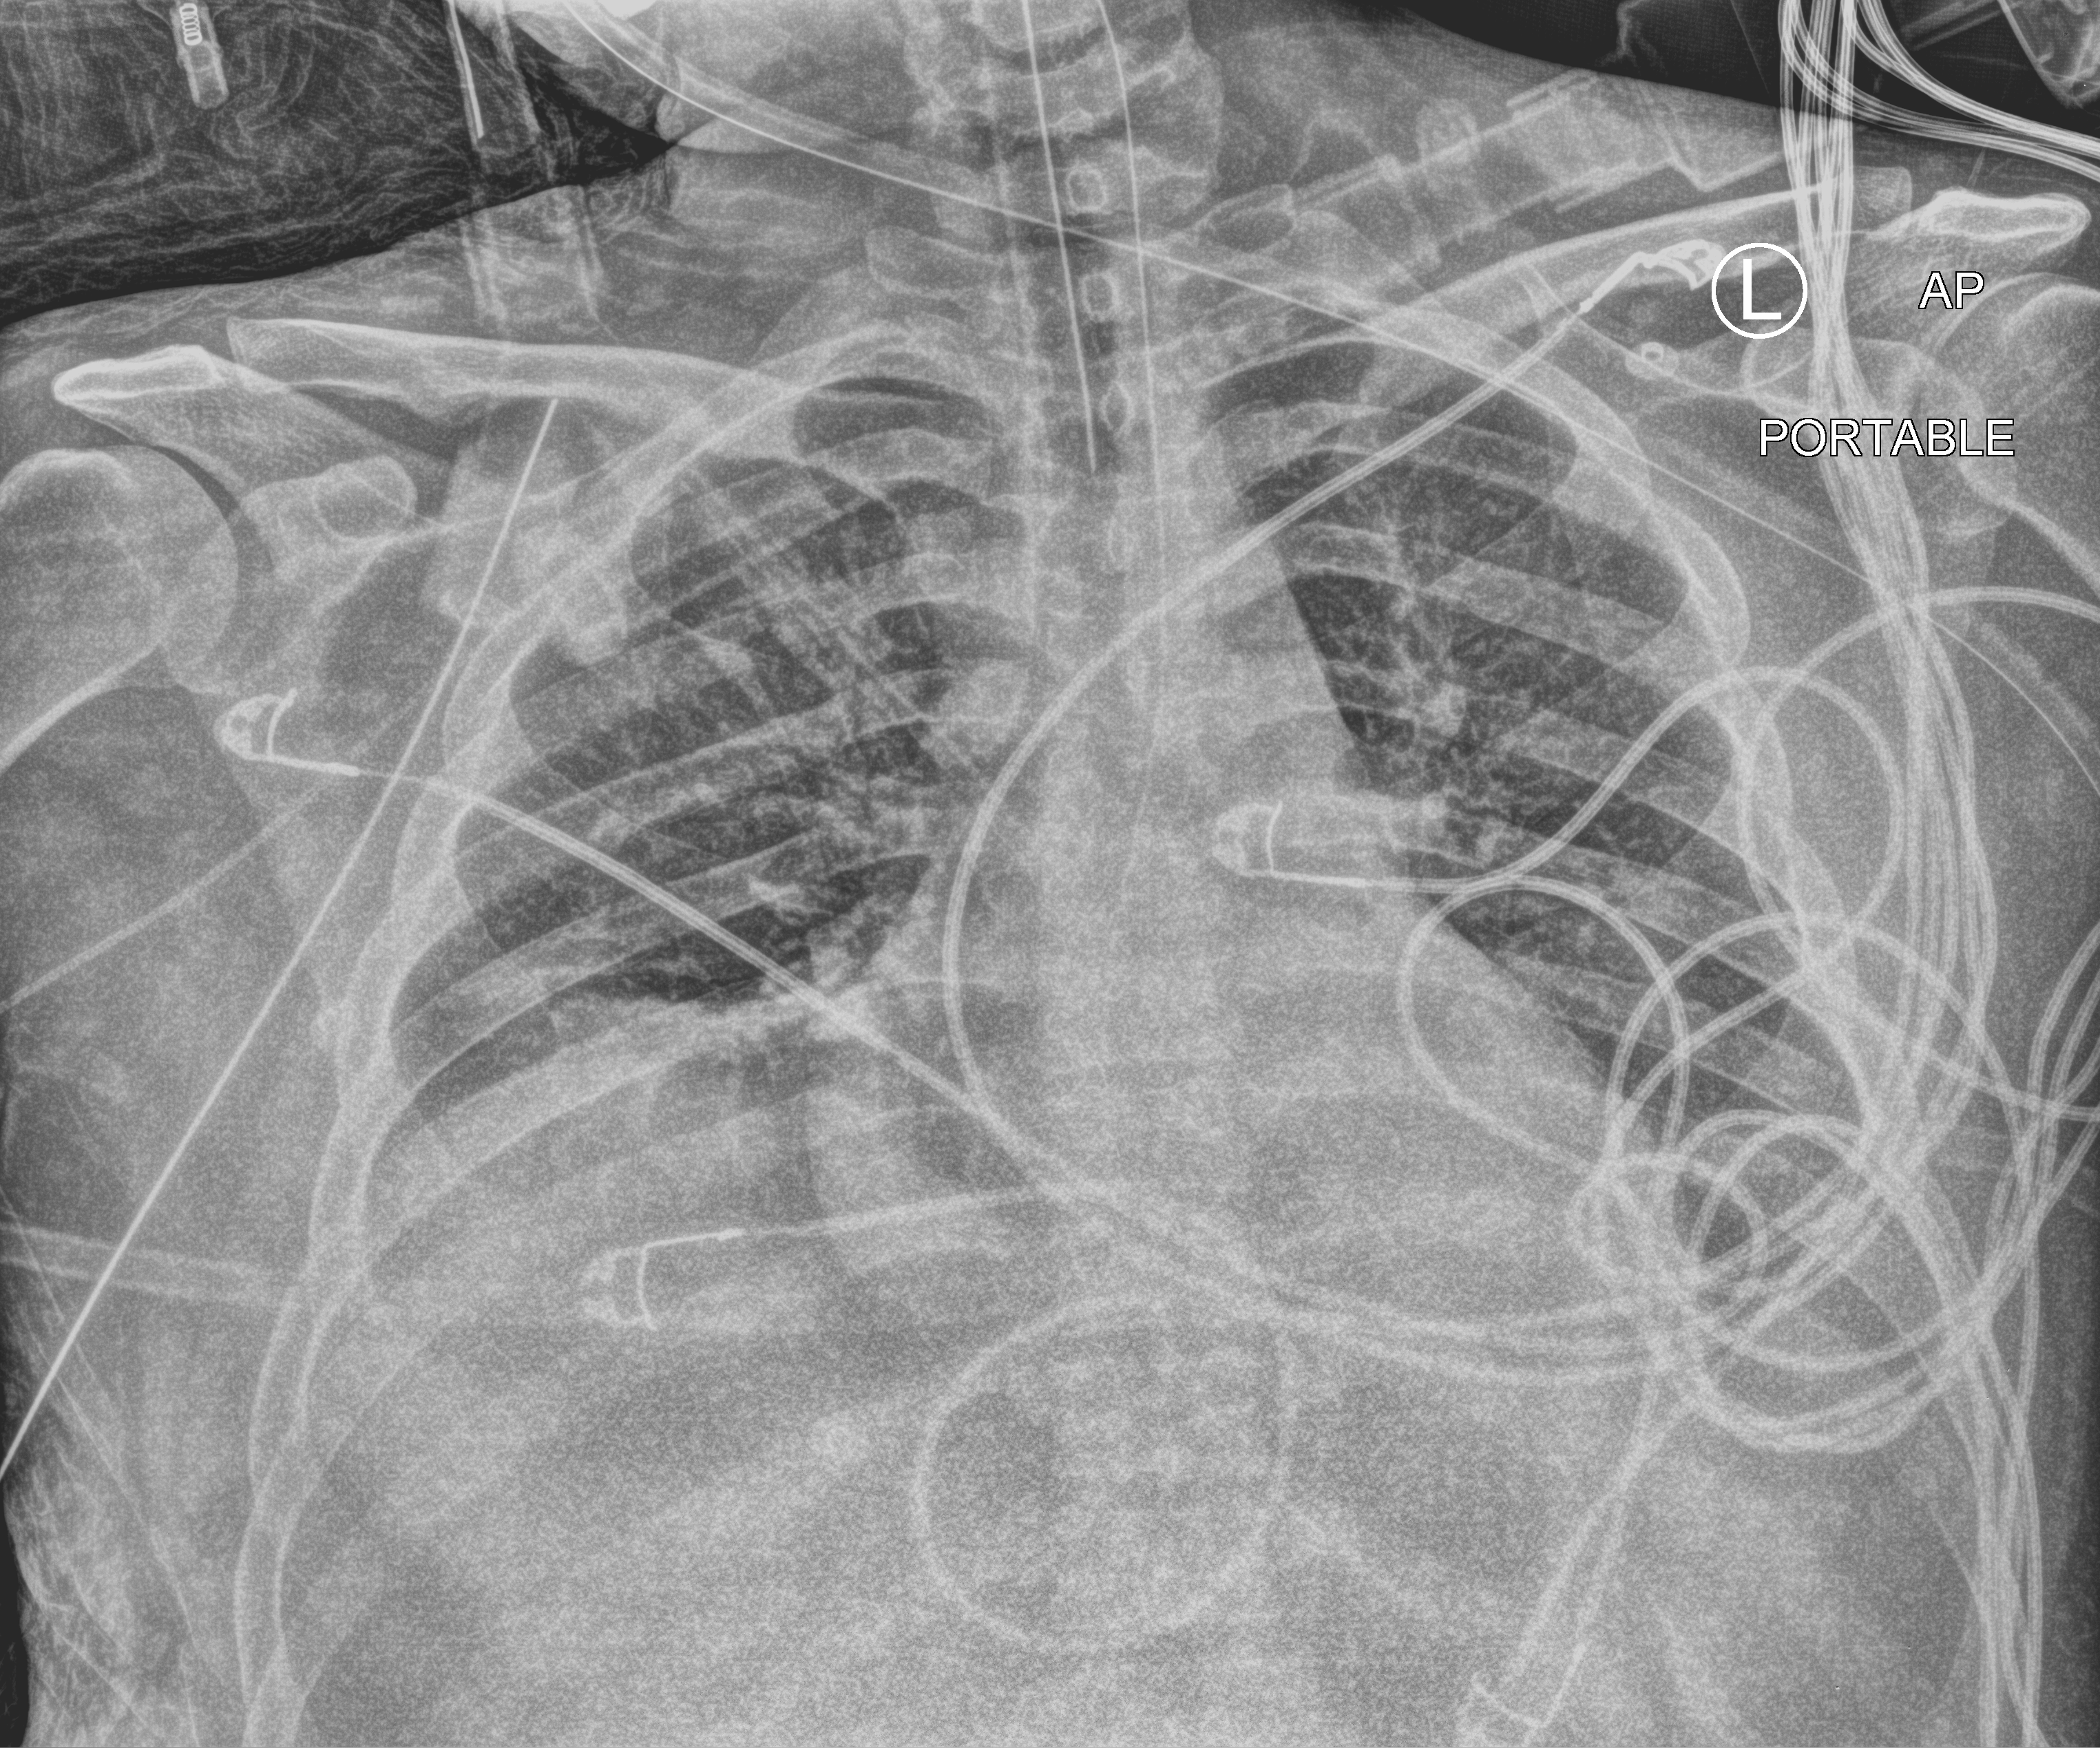
Bedside chest radiograph (computed radiography); anteroposterior (AP) projection. Patient hospitalised with COVID-19; male, aged 18–59 years.
Hospital-stay facts (about this admission, not read from this image; timing relative to this image not recorded):
- other chronic lung disease (admission record): no